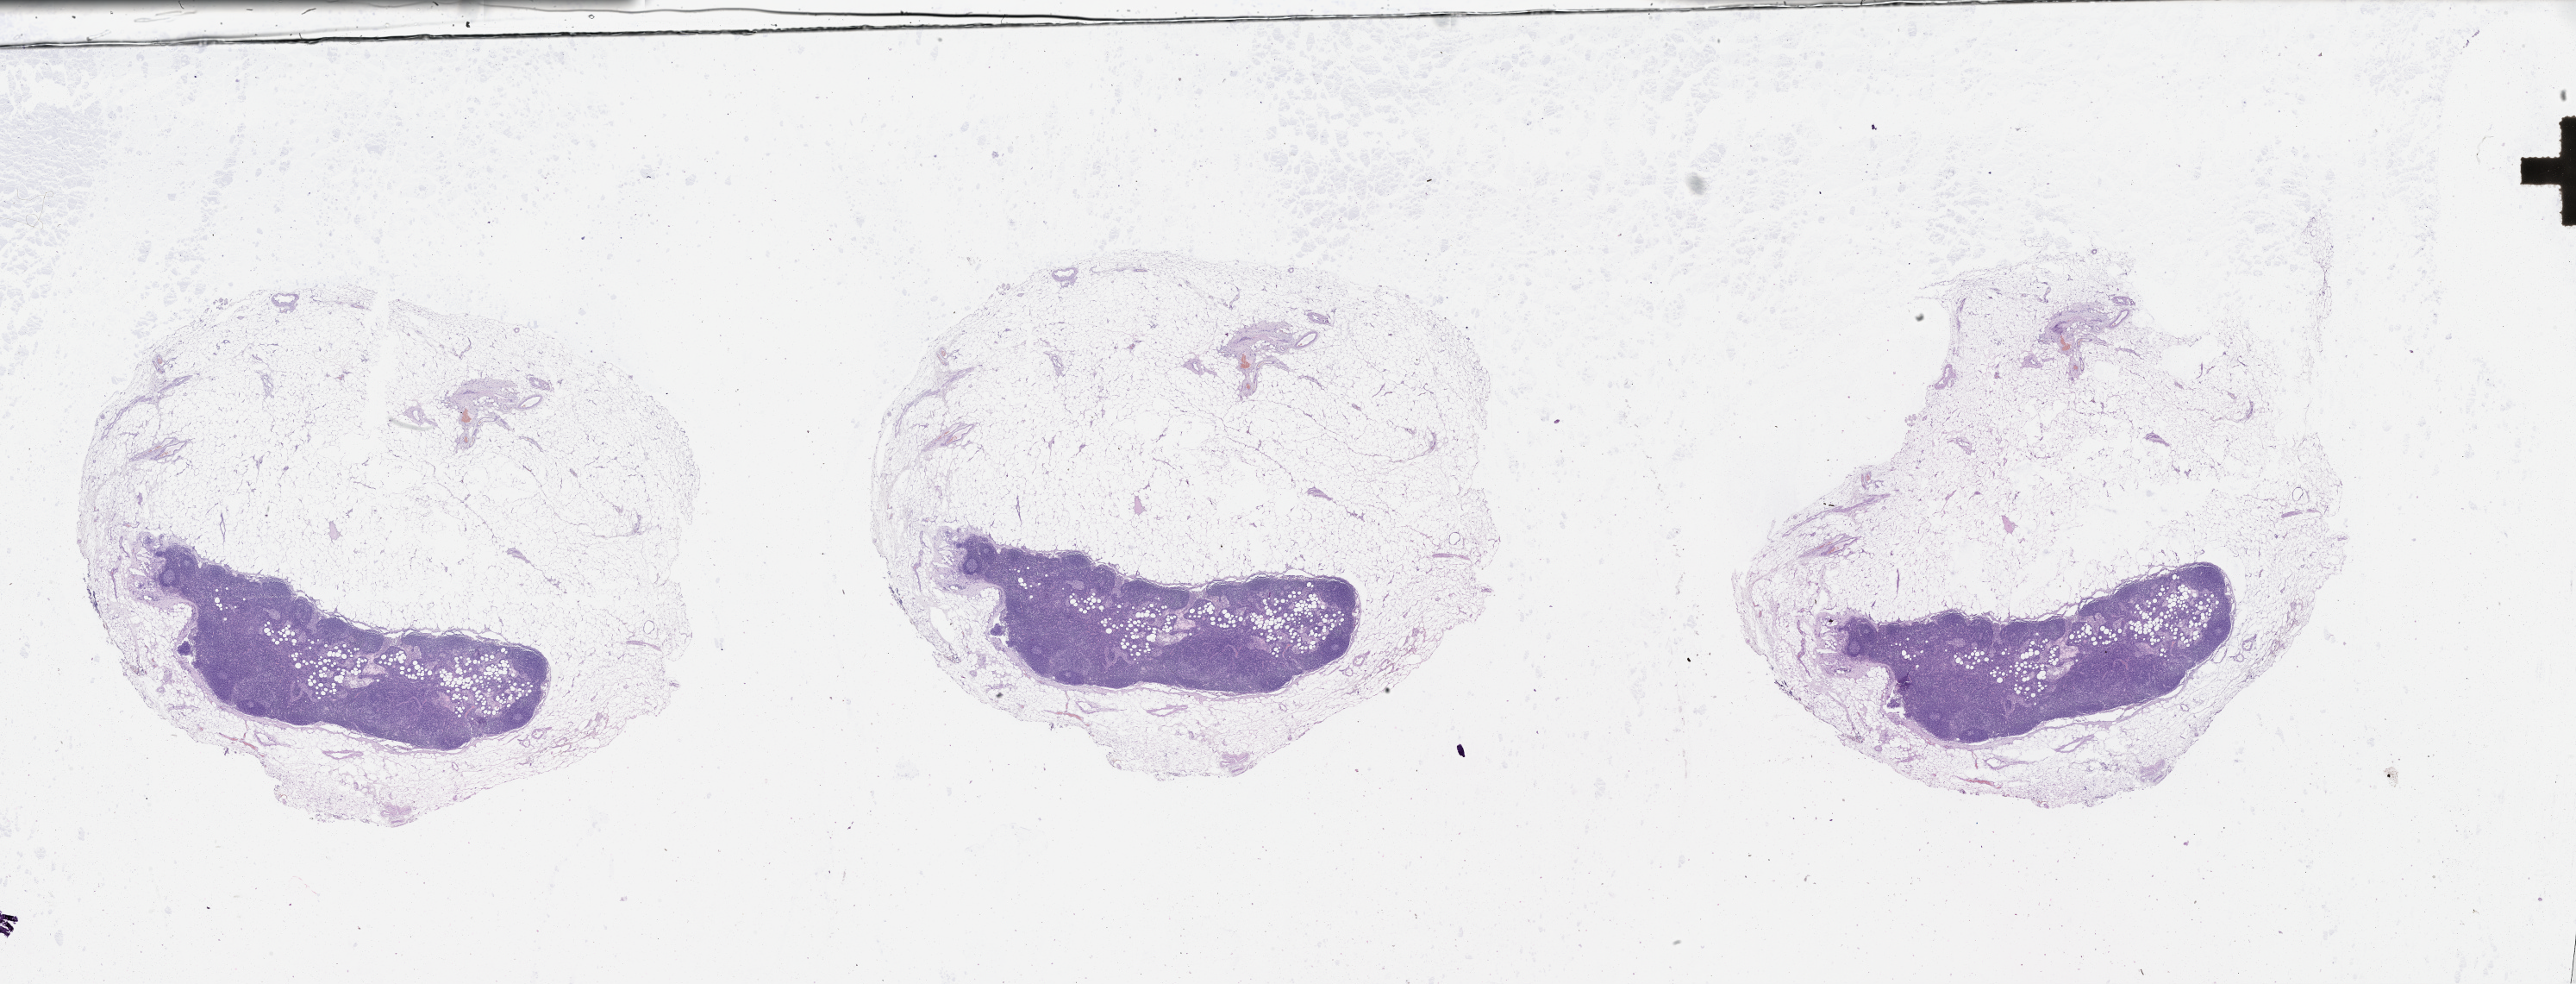
Whole-slide histology image, Hematoxylin and eosin (H&E) stained — low-resolution overview of the scanned area, about 48.1 x 18.4 mm (acquisition: 20x scan); normal (non-tumour) tissue sample, sampled site: lymph node. Patient: female, age 62 years.
This section: normal (non-tumour) tissue from the same patient. Patient diagnosis: Malignant melanoma, NOS.